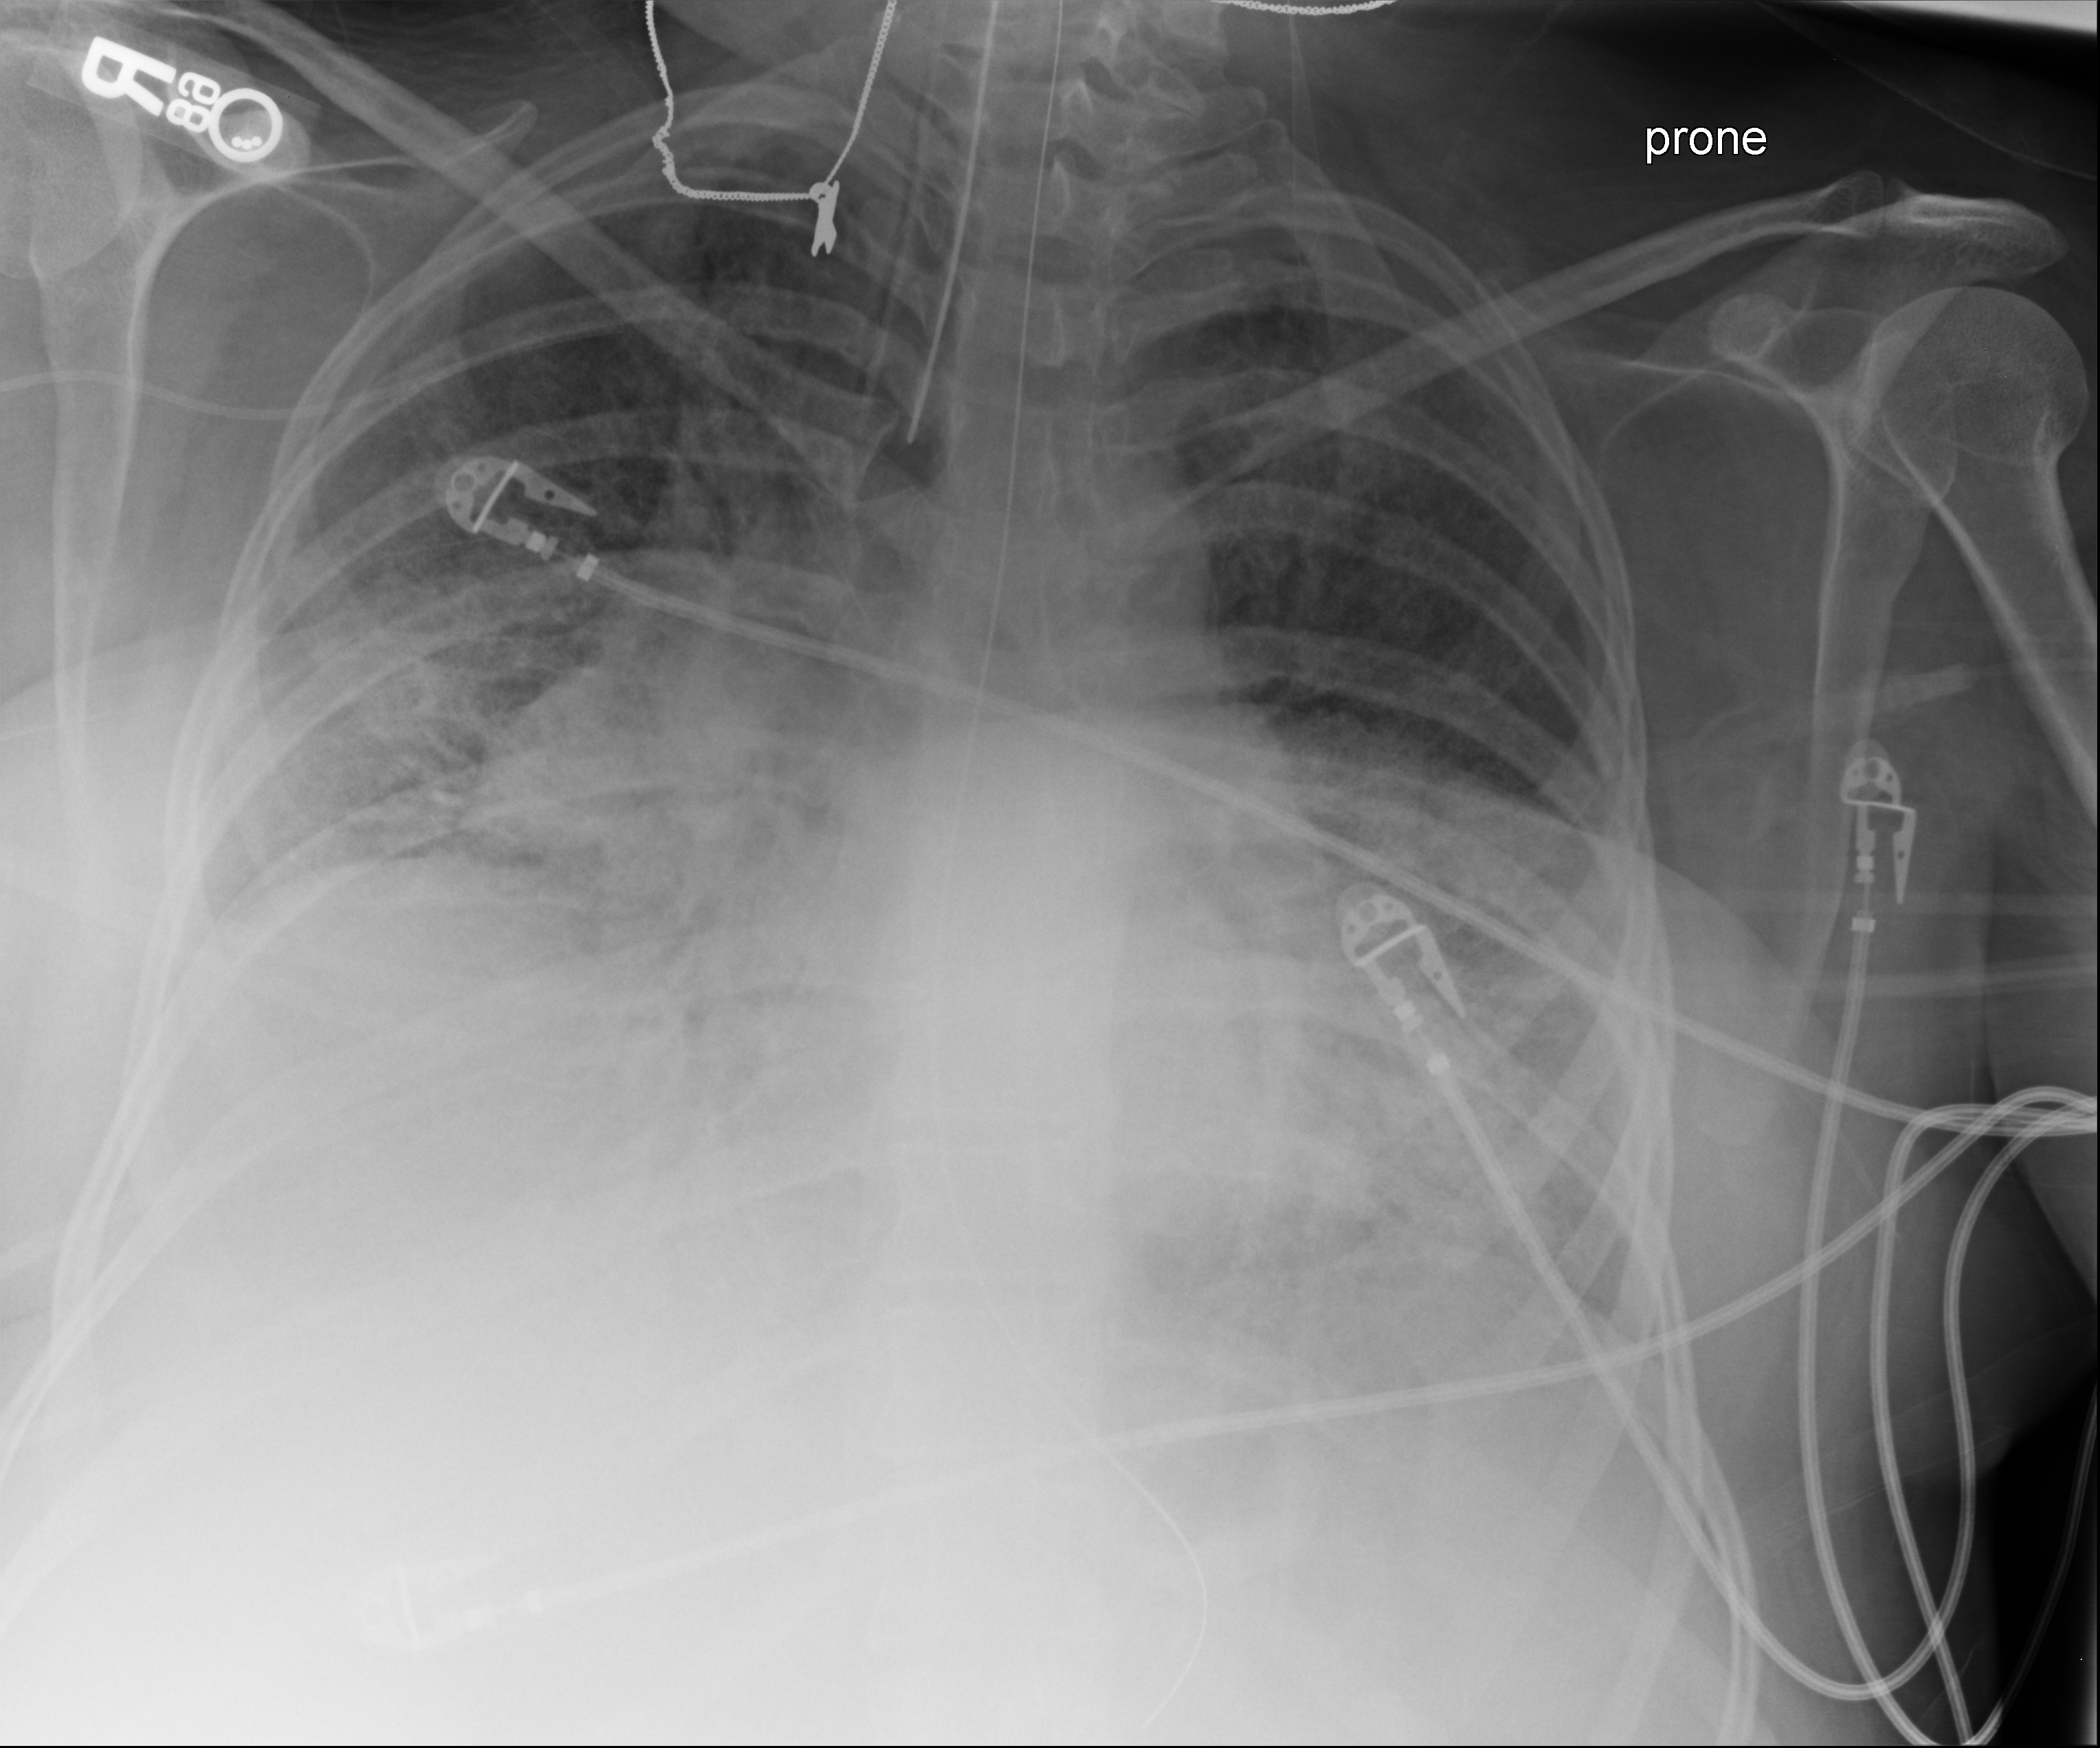
Portable chest radiograph. Female patient hospitalised with COVID-19, age 18–59 years.
Admission-level facts for this patient (not findings on this image; timing relative to this image not recorded): COPD (admission record): no.